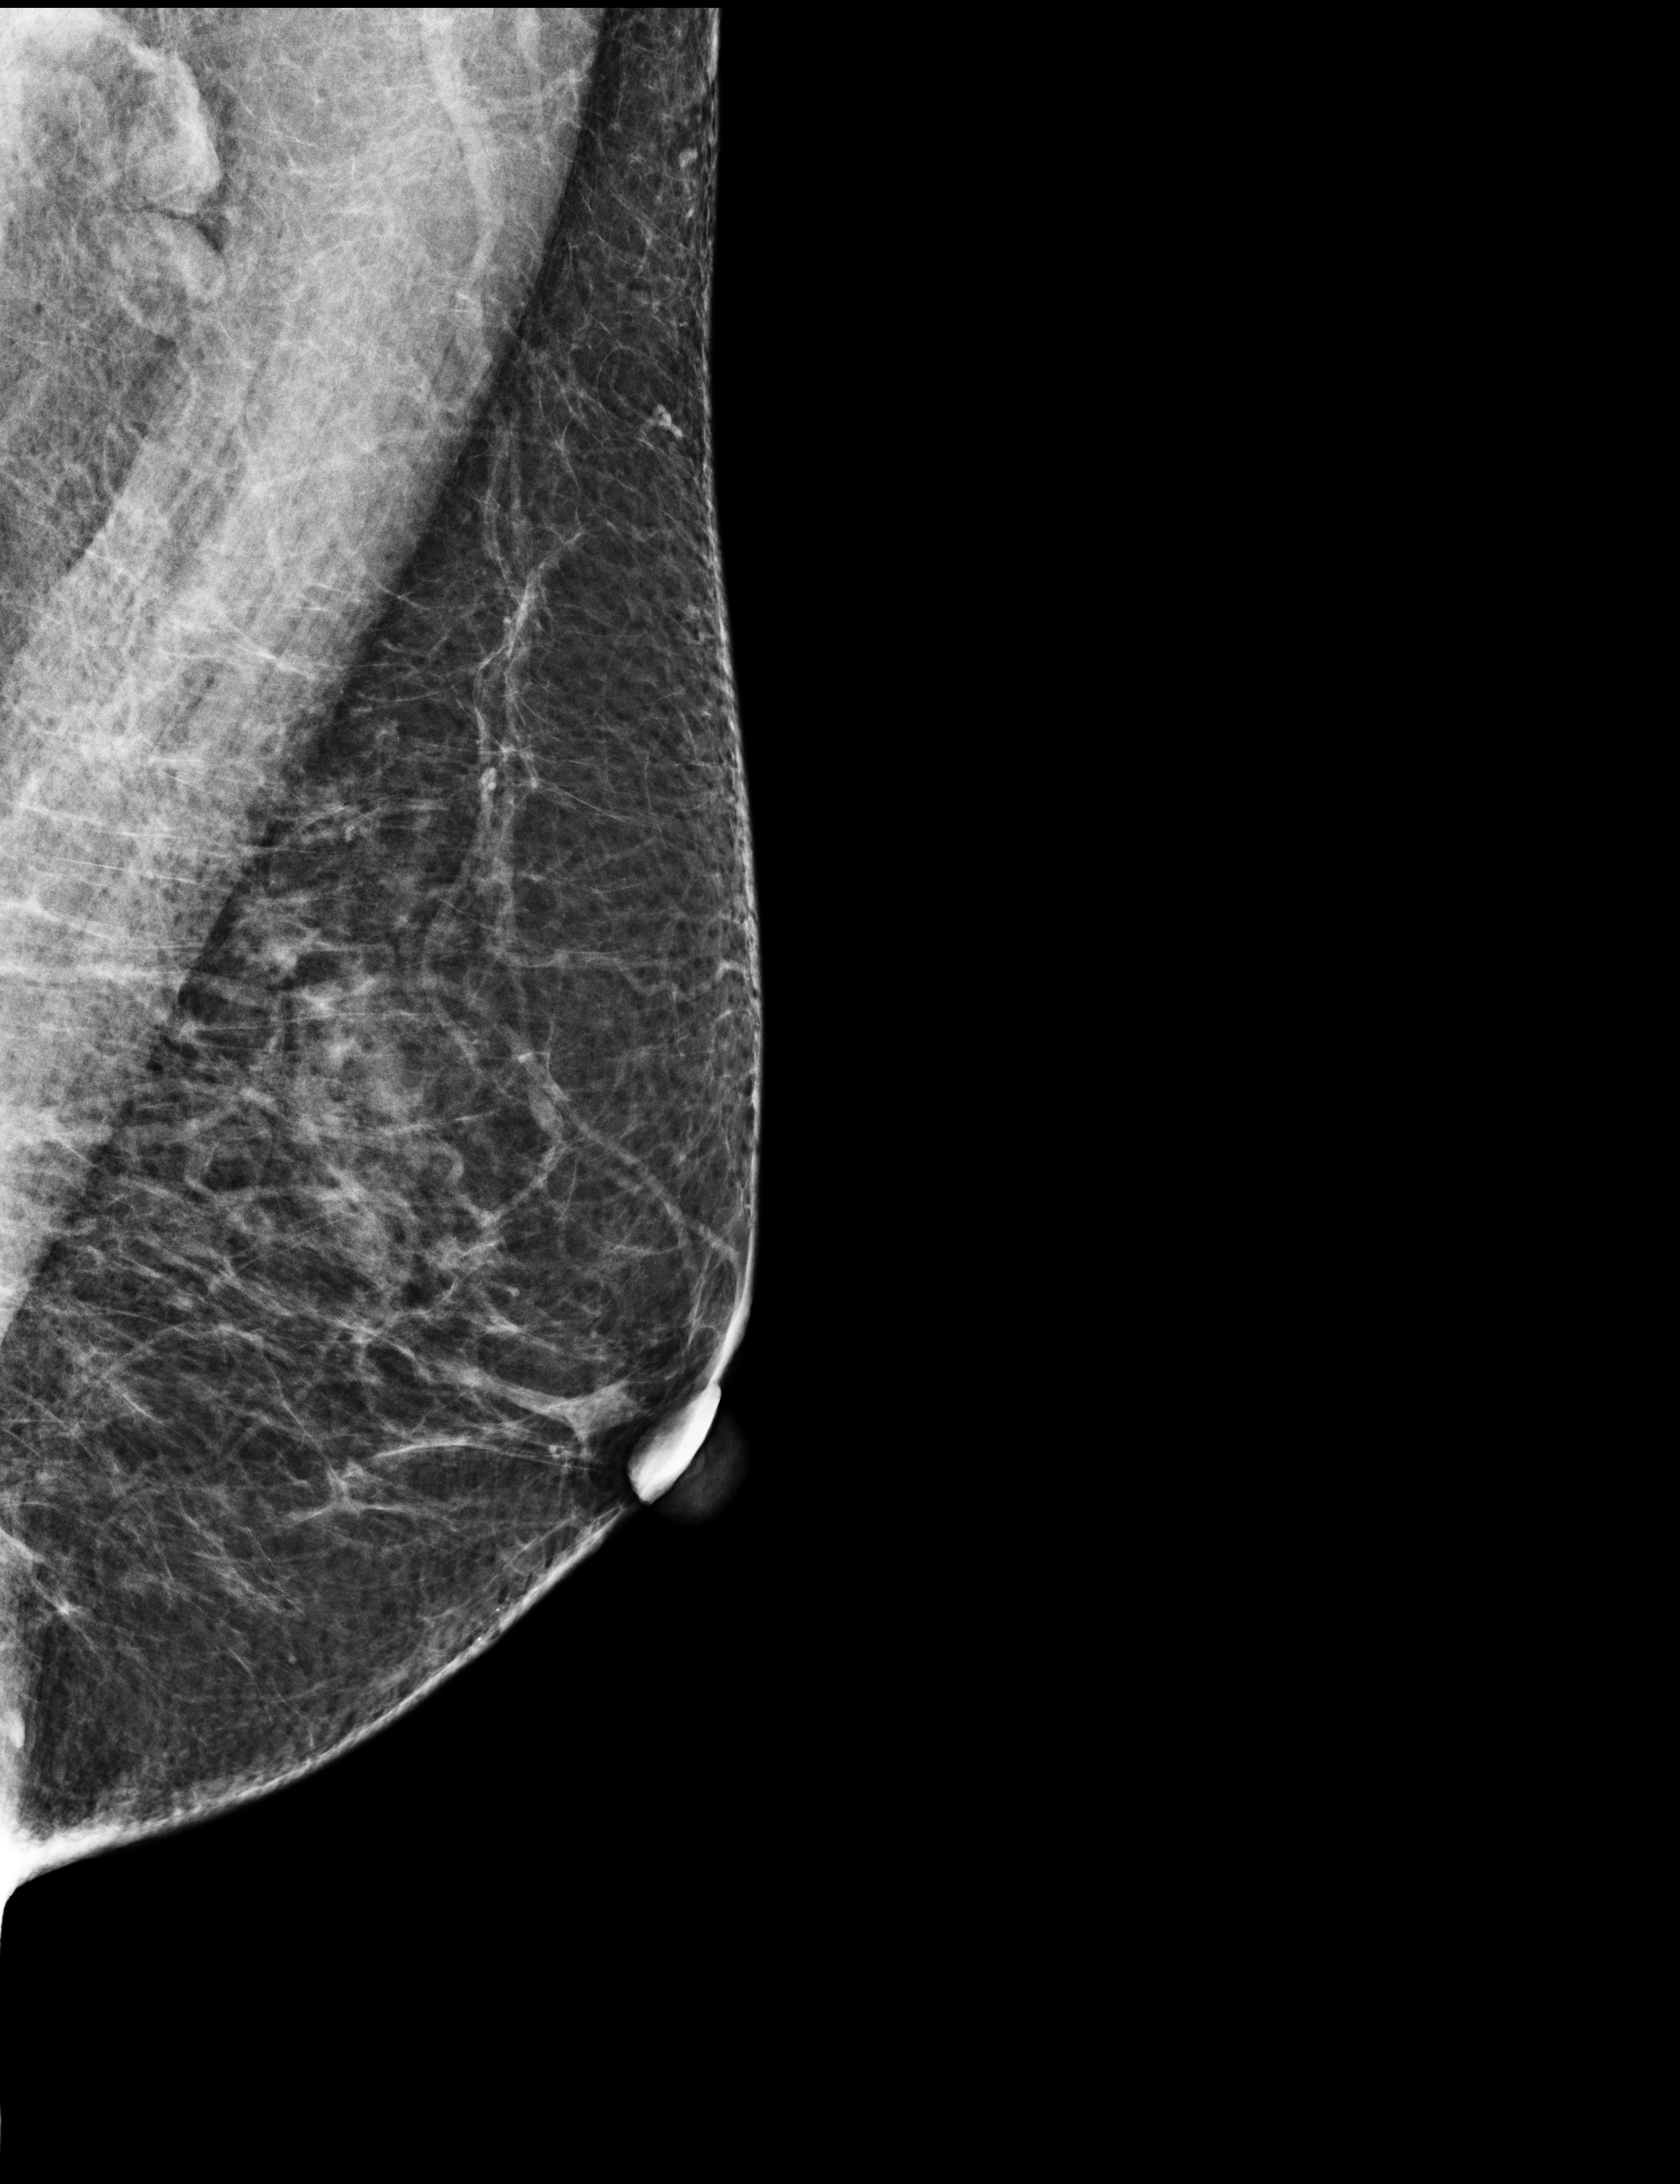
Digital mammogram (FFDM), left breast, MLO view, annual screening mammography examination, compressed breast thickness 57 mm, system: Selenia Dimensions. Patient: female, 61 years.
Breast density at the screening exam (both breasts): heterogeneously dense (BI-RADS density category c). Final BI-RADS assessment for this screening round (tomosynthesis exam, both breasts): category 2. Recall: recalled for additional imaging after this screen.